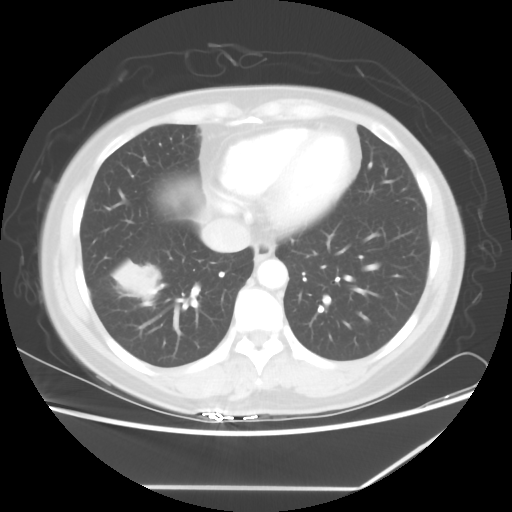
Chest CT, one axial slice; position 21 of 60 along the scan axis; reconstruction kernel STANDARD; 100 kVp; lung window (W 1500 / L -600 HU); 512 × 512 image matrix, field of view 374 × 374 mm. Patient: female, 42 years. Case-level facts recorded for this patient, not image findings: clinical TNM (as recorded): T2 N1 M0.
Outlined on this slice (rectangle marked by the reading radiologist):
- lung tumour (recorded histology: adenocarcinoma): bounding box <110,257,166,309> (left, top, right, bottom; pixels)